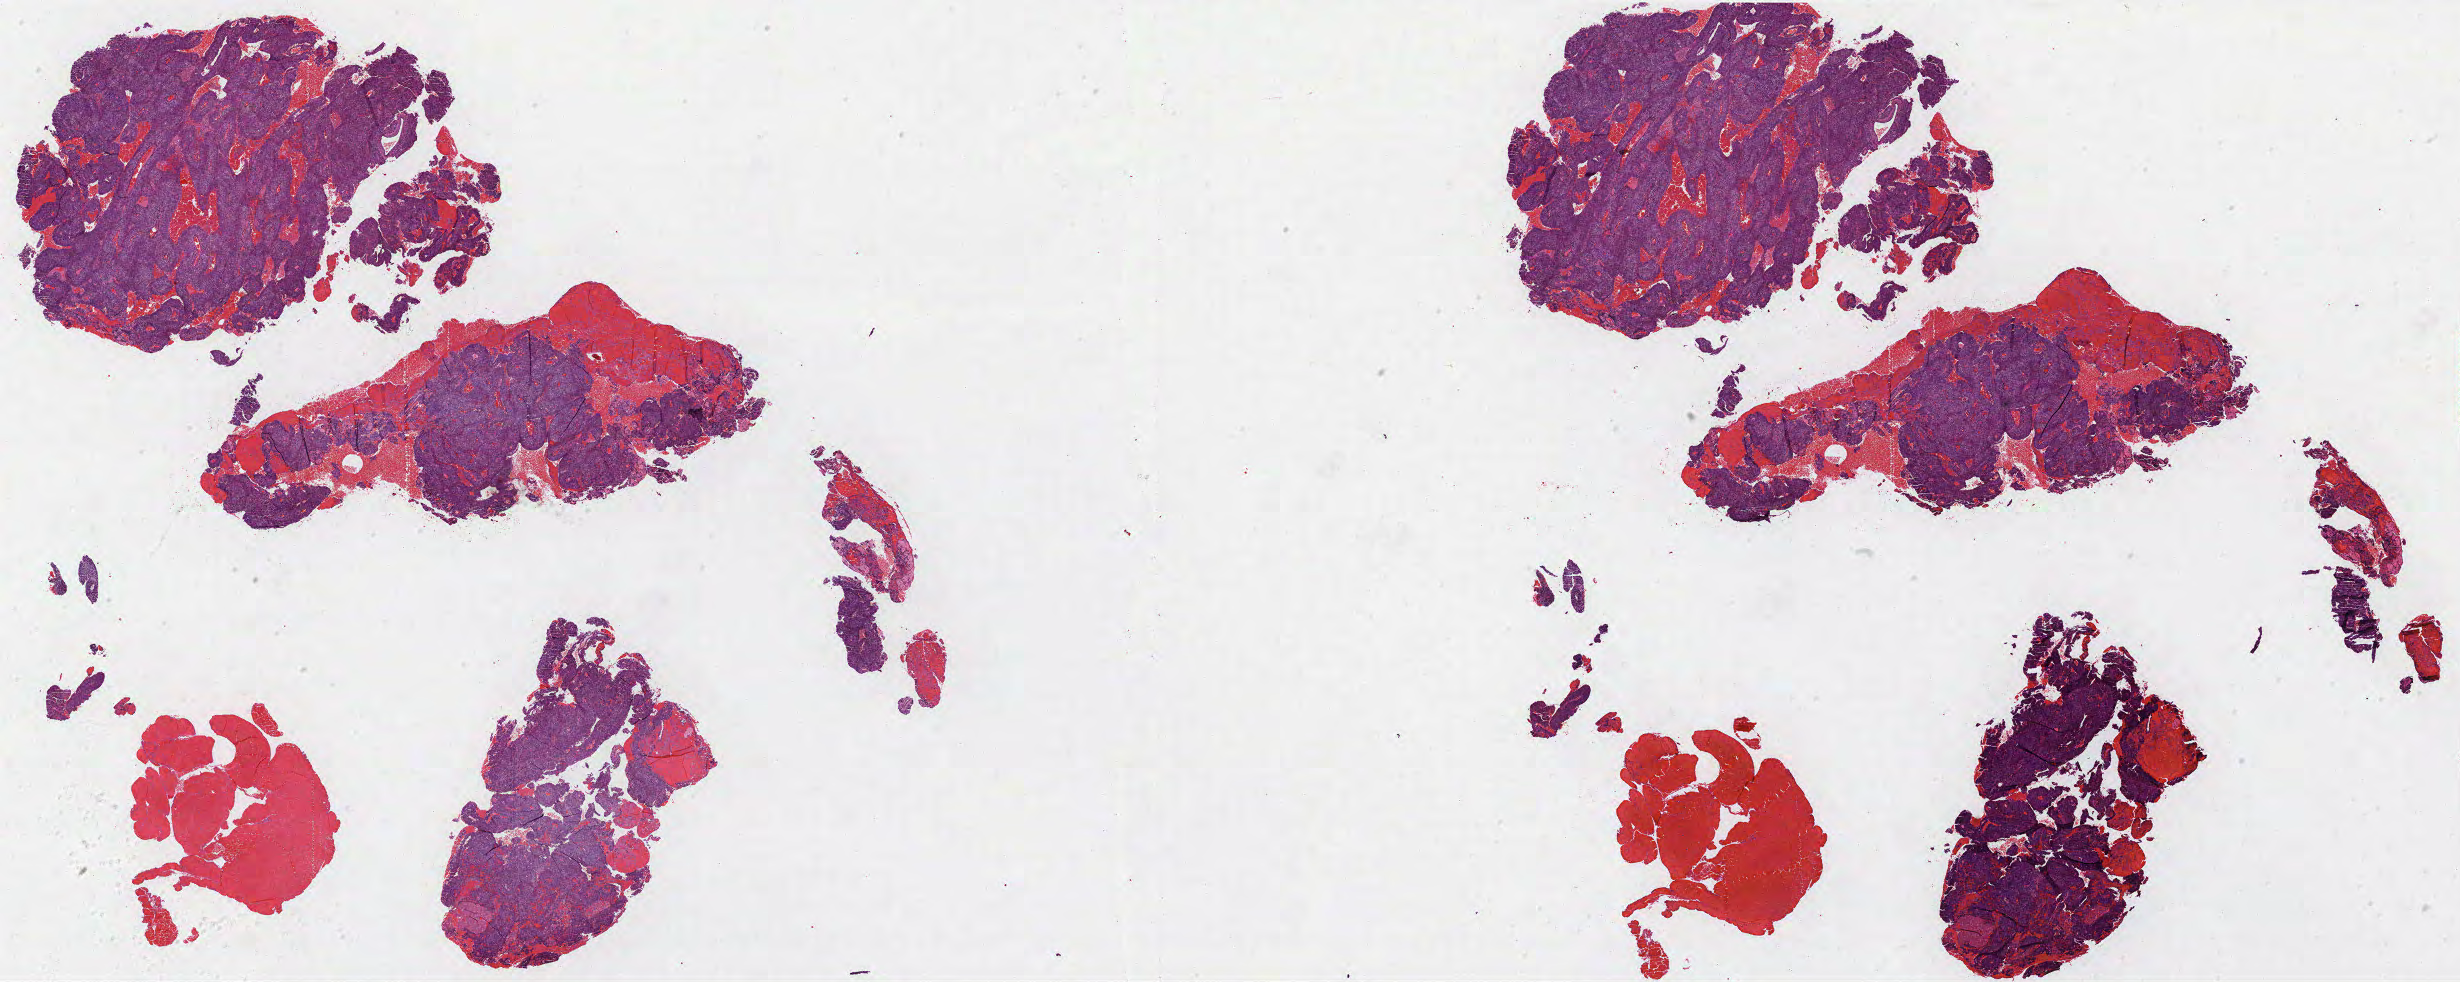
Digitized H&E tissue section (whole slide) — low-resolution overview of the scanned area, about 39.4 x 15.7 mm, formalin-fixed paraffin-embedded (FFPE) diagnostic section, primary tumour sample from the cervix. Female patient; age at initial diagnosis 74 years.
Diagnosis: Squamous cell carcinoma, NOS (cervix uteri). FIGO stage: IB.